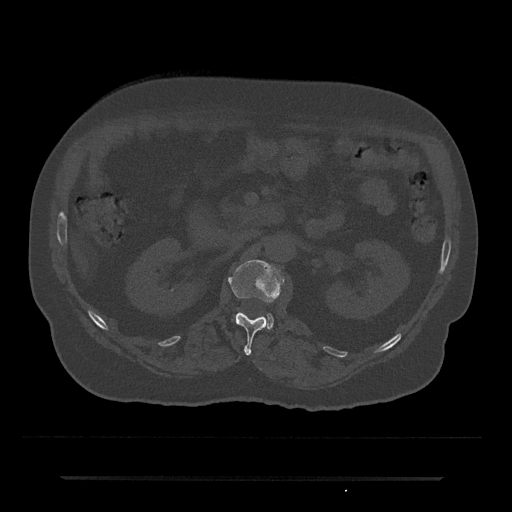
CT including the spine, one axial slice; position 55 of 797 along the scan axis; reconstruction kernel Br40s/3; bone window (W 1800 / L 400 HU); 0.5 mm slice thickness; 512 × 512 image matrix, field of view 437 × 437 mm. Male patient, age 69 years. From the clinical record (not read from this slice): primary cancer: prostate.
Structures marked on this image (semi-automatic segmentation, software-assisted and operator-edited):
- L1 vertebra: box from (x=229, y=260) to (x=284, y=355) px
- L2 vertebra: (x=266, y=313)–(x=274, y=329)